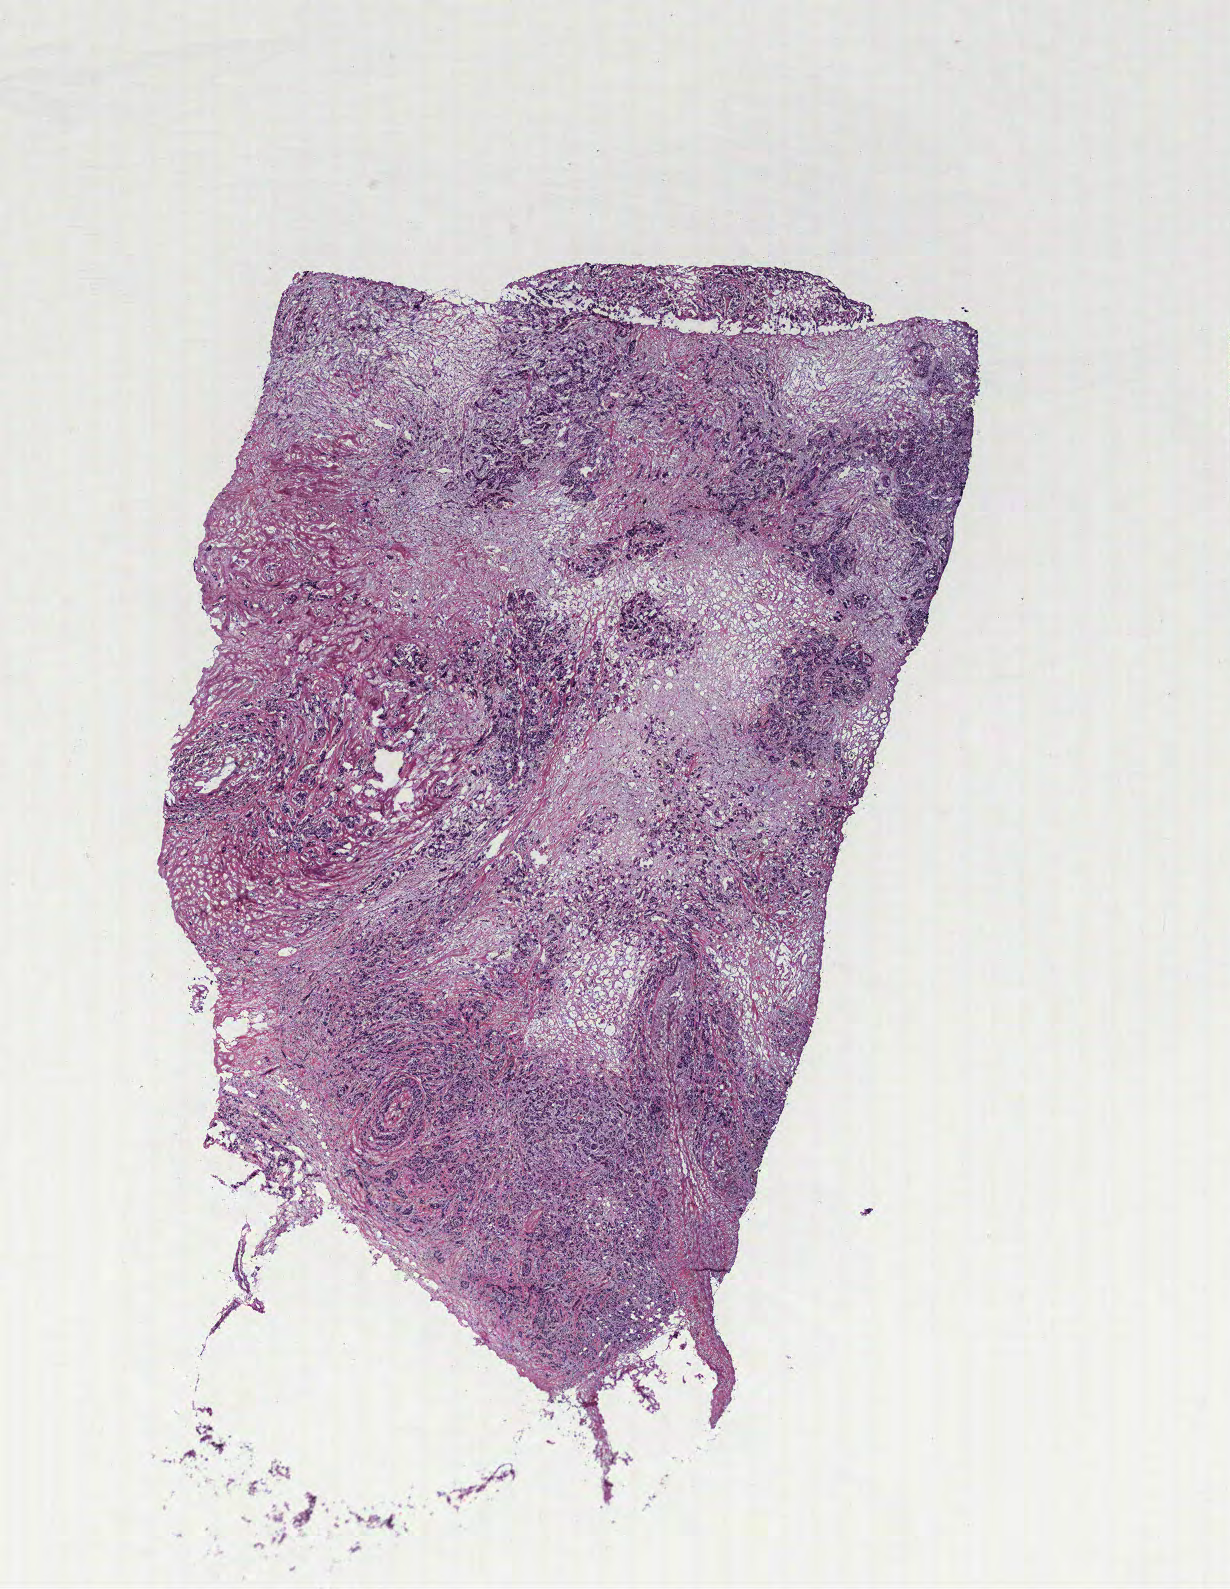
Digitized Hematoxylin and eosin (H&E) stained tissue section (whole slide), low-resolution overview of the scanned area, about 9.8 x 12.7 mm. Tumour tissue sample, breast. Patient: female, aged 90 or older.
Diagnosis: Infiltrating duct carcinoma, NOS.